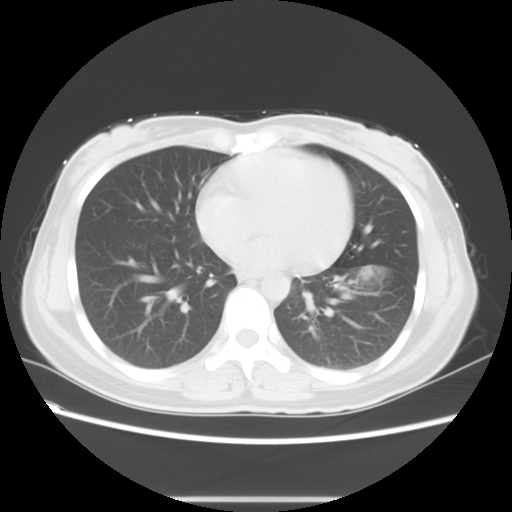
Chest CT, one axial slice. Position 25 of 56 along the scan axis. Reconstruction kernel STANDARD. 120 kVp. Lung window (W 1500 / L -600 HU). 5 mm slice thickness. 512 × 512 image matrix, field of view 350 × 350 mm. Female patient, age 41 years. From the clinical record (not read from this slice): clinical TNM (as recorded): T1c N3 M1b.
Outlined on this slice (bounding box drawn by a radiologist):
- lung tumour (recorded histology: adenocarcinoma): bounding box (x1, y1, x2, y2) in pixels: (352, 258, 395, 307)